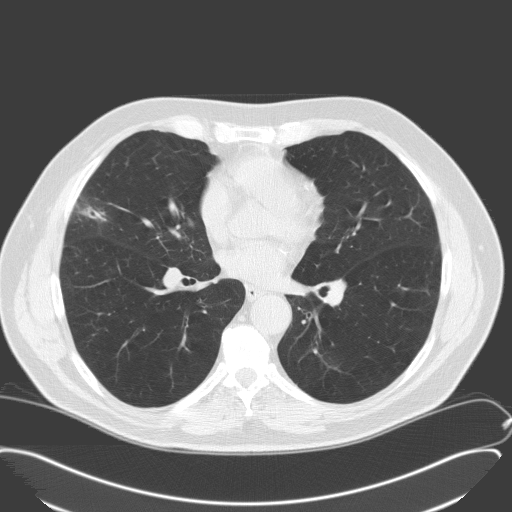
Low-dose screening chest CT, axial slice, second screening round (one year after baseline), lung window (W 1500 / L -600 HU), slice 90 of 175 in the series, 512 × 512 image matrix. Male, age 65 years at enrolment. Former smoker at enrolment.
- Lesion marked by an expert reader, box from (x=52, y=190) to (x=117, y=244) px.
- Screening reader's record for this exam: no non-calcified nodule ≥4 mm recorded.